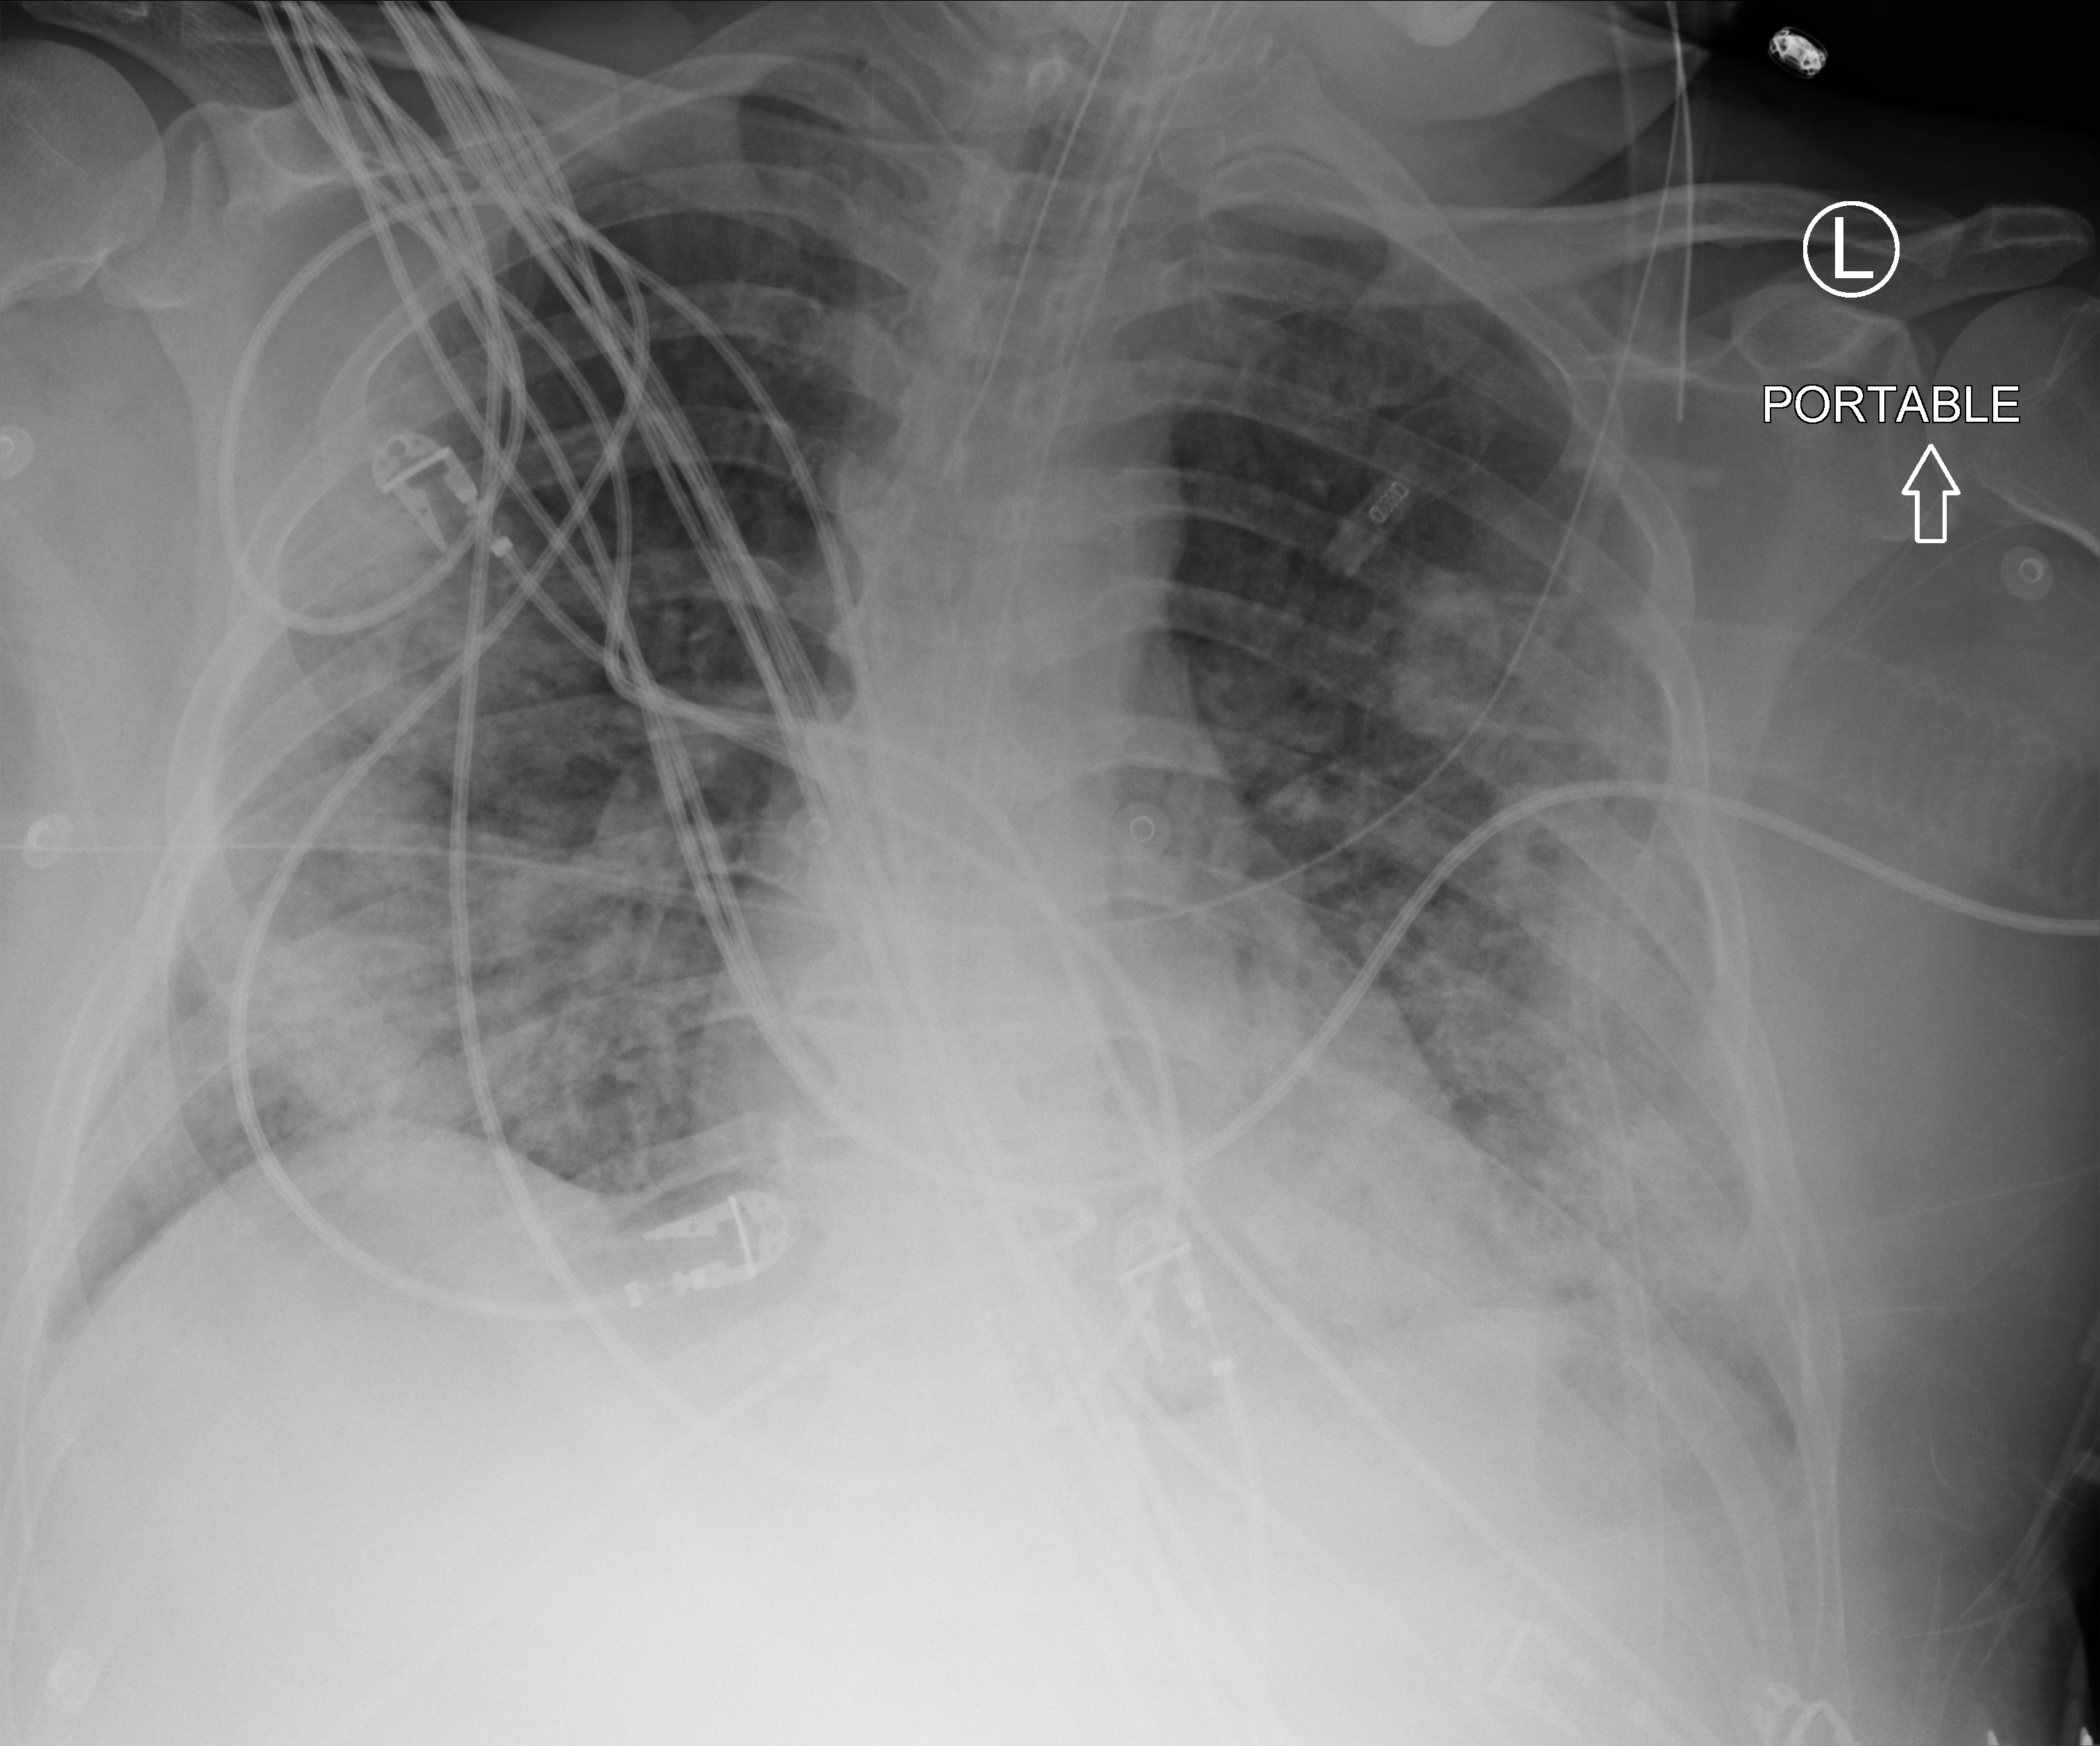
Chest X-ray (portable); anteroposterior (AP) projection. Patient hospitalised with COVID-19; male, aged 18–59 years.
From the hospital-stay record, not from the radiograph (when in the stay this image was taken is not recorded):
- COPD (admission record): no